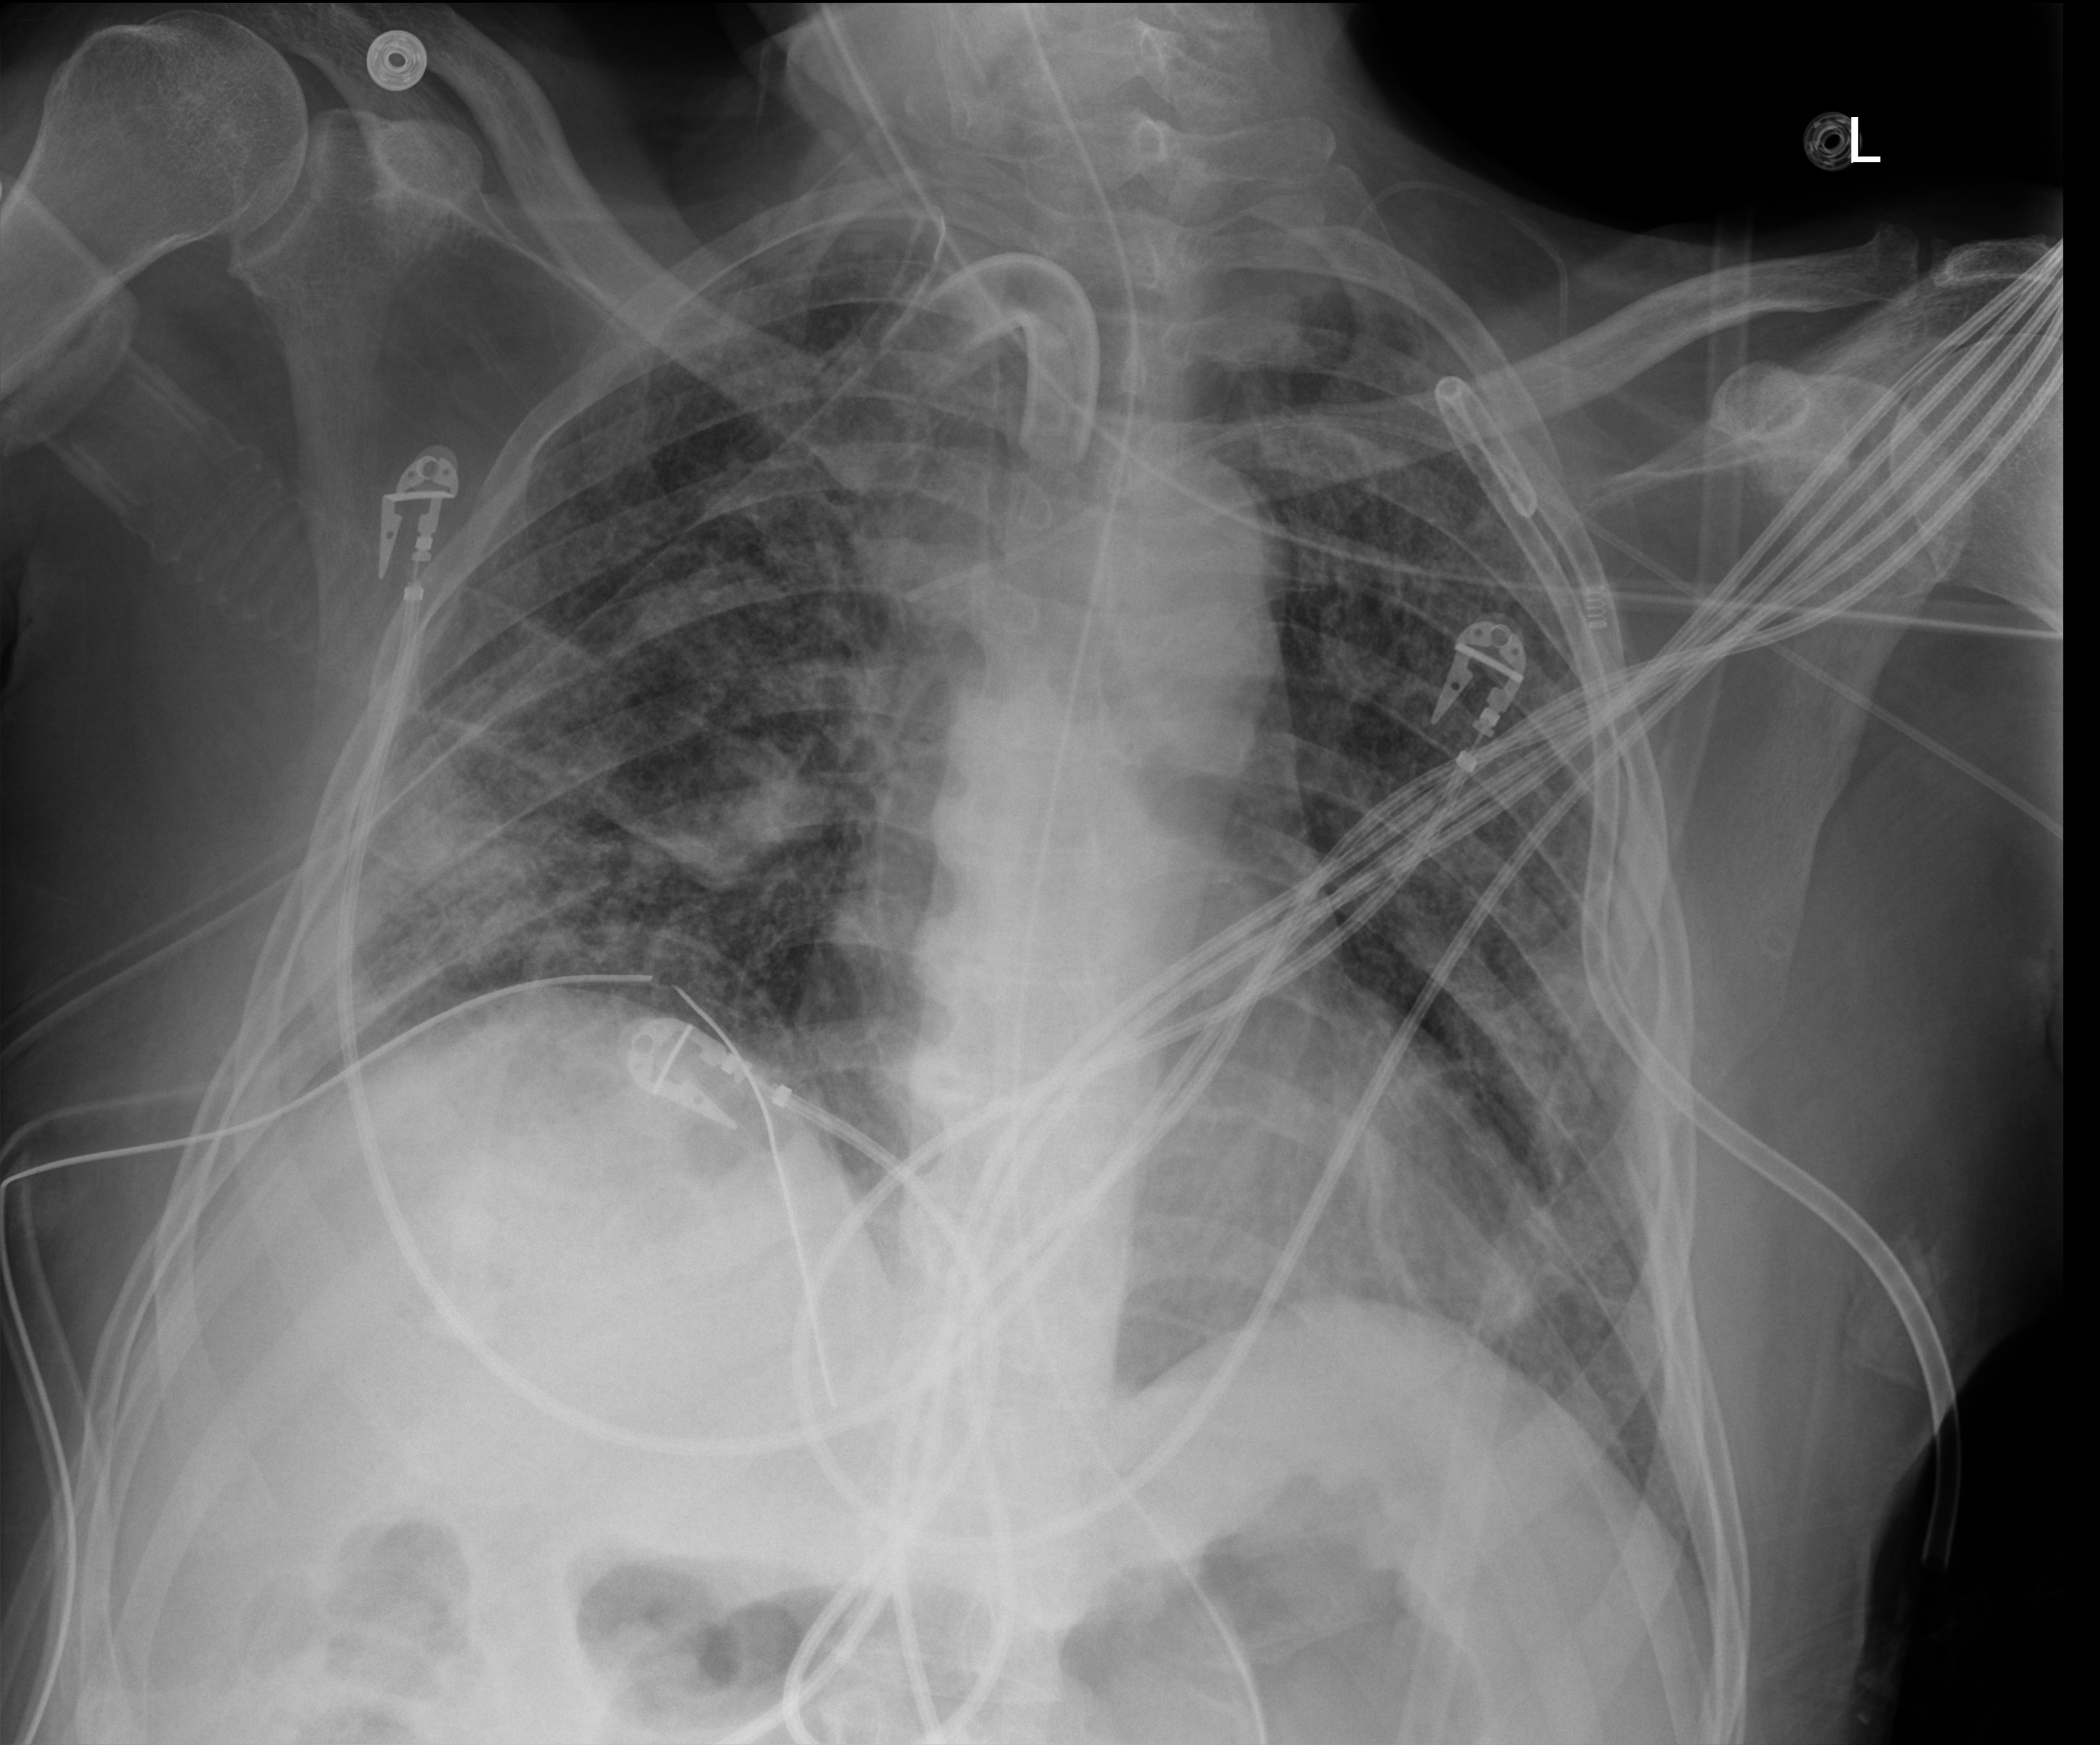
Portable chest radiograph. Patient hospitalised with COVID-19; male, aged 18–59 years.
Hospital-stay facts (about this admission, not read from this image; timing relative to this image not recorded): mechanically ventilated during this hospital stay: yes; admitted to intensive care during this hospital stay: yes; chronic kidney disease (admission record): no.